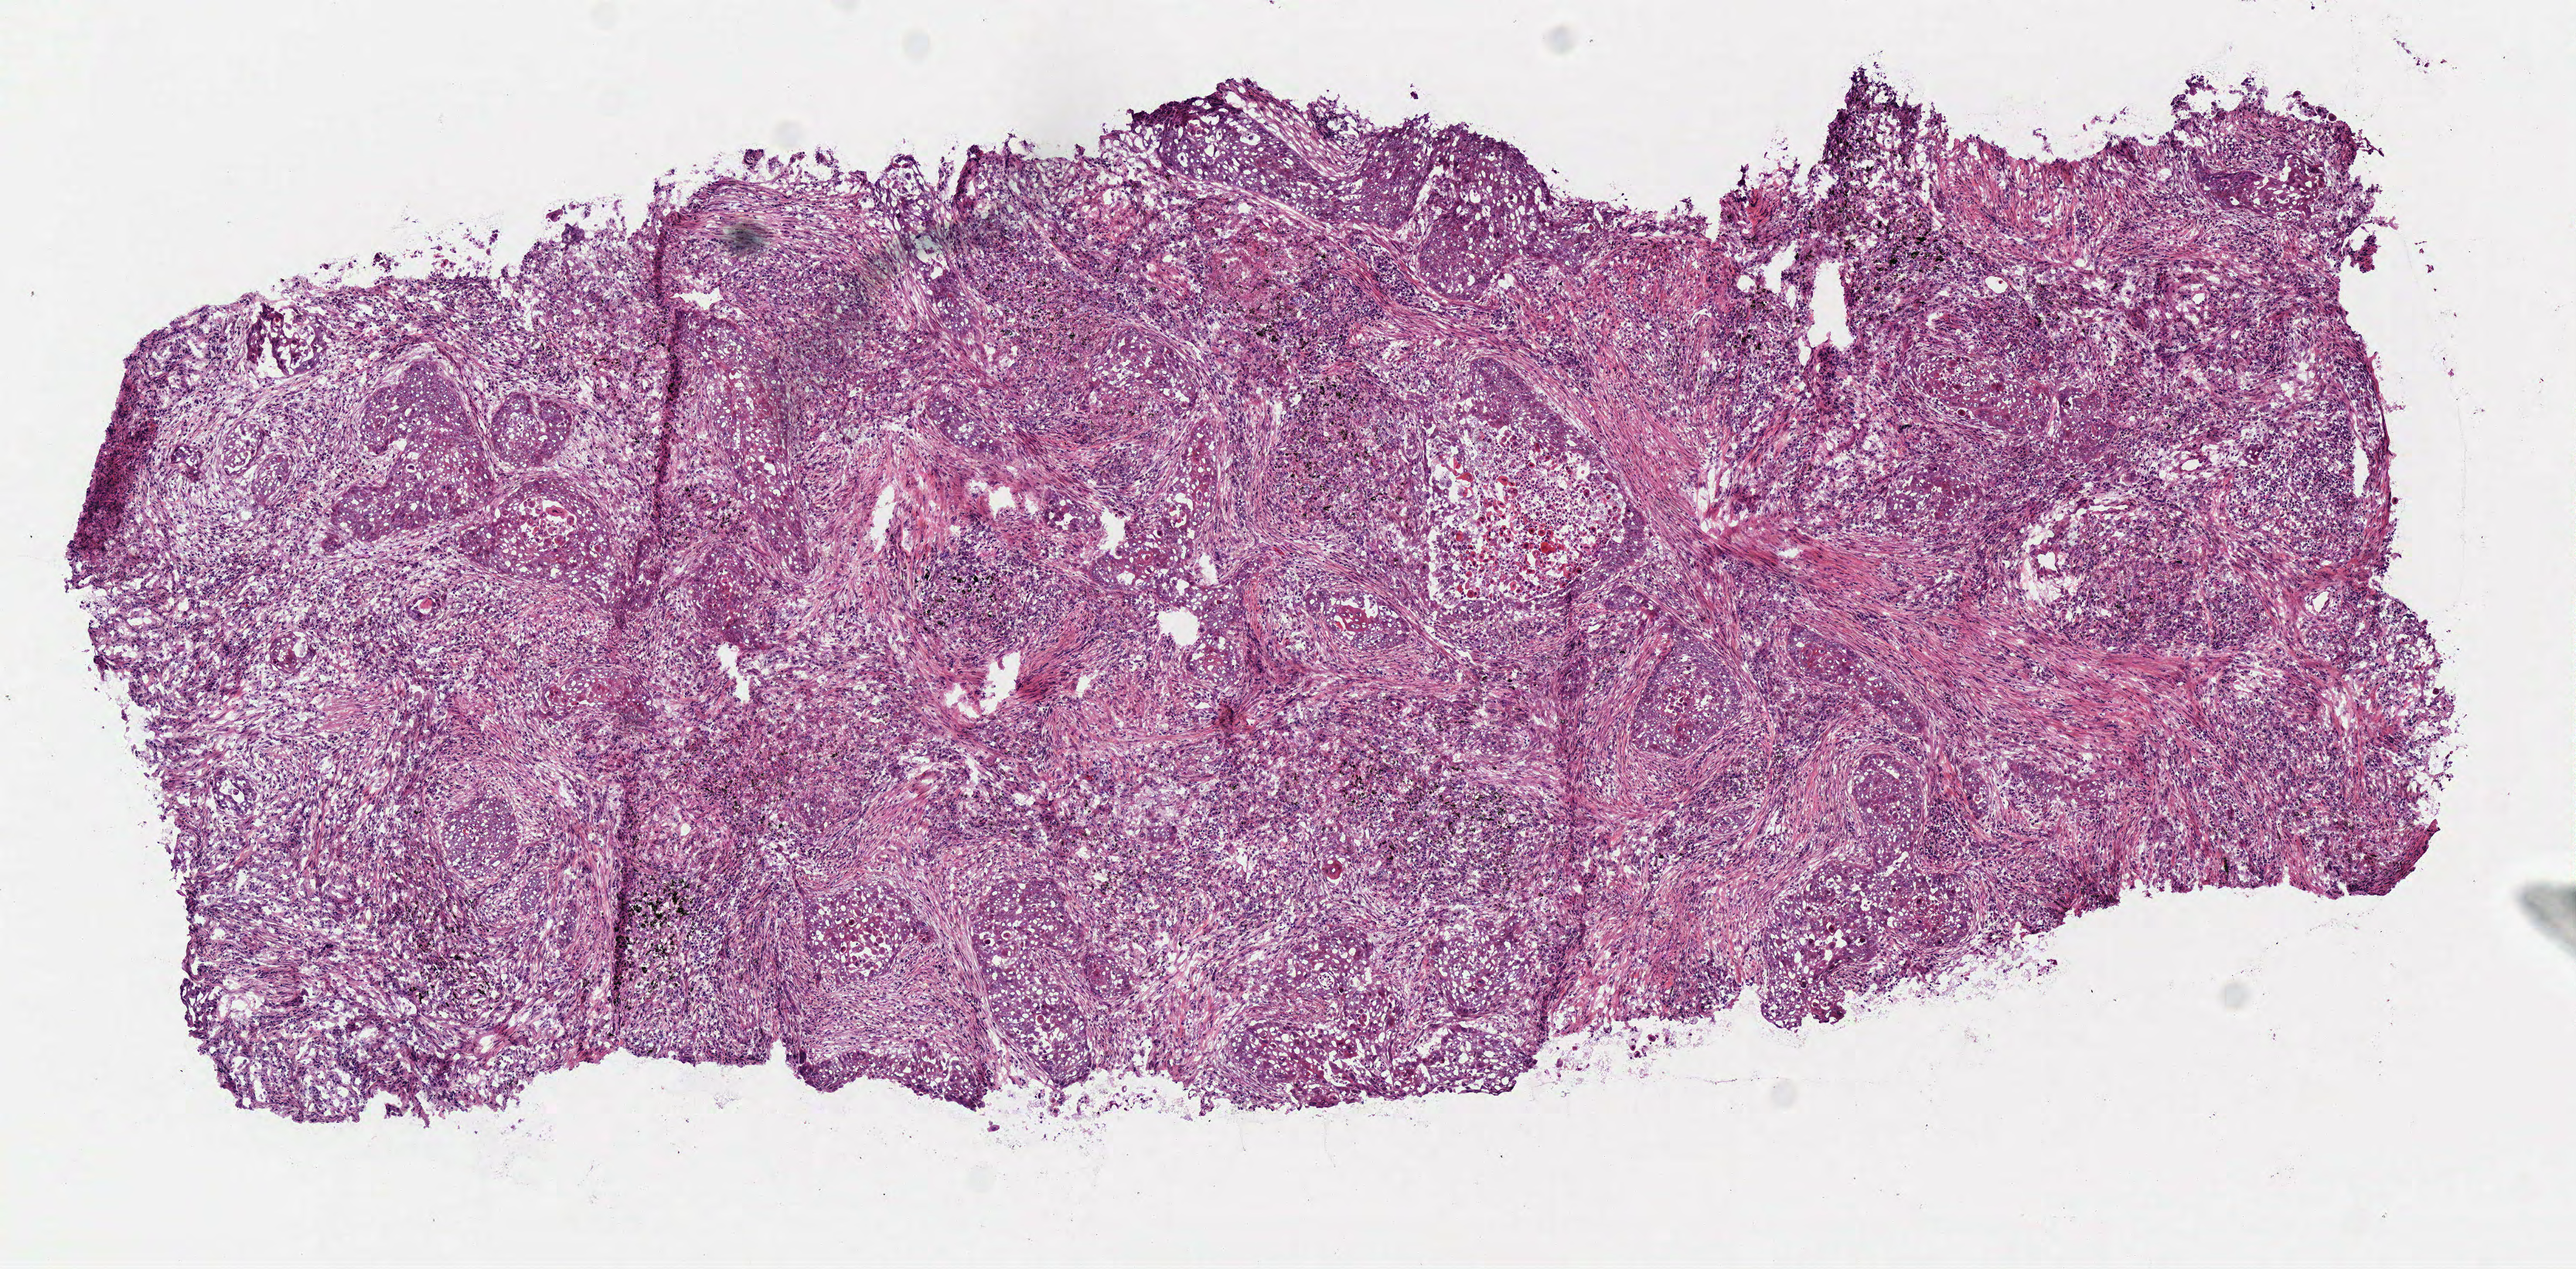
Digitized H&E tissue section (whole slide) — low-resolution overview of the scanned area, about 6.6 x 3.2 mm (slide scanned at 40x); frozen section from the top of the tissue portion; lung, primary tumour sample. Male patient; age at initial diagnosis 74 years. Pathologist review of this section (percent, as recorded): tumour cells 65%, tumour nuclei 65%, normal cells 0%, stromal cells 25%, necrosis 10%. Infiltration values recorded for this section: lymphocyte infiltration 25%, monocyte infiltration 0%, neutrophil infiltration 0%.
• AJCC pathologic stage: IA
• histologic diagnosis: Squamous cell carcinoma, NOS (upper lobe, lung)